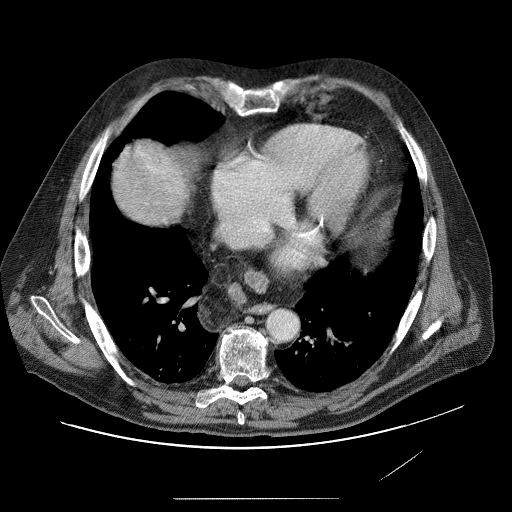
Contrast-enhanced abdominal CT (liver protocol), one axial slice; position 80 of 89 along the scan axis; soft-tissue window (W 400 / L 40 HU); 512 × 512 image matrix, field of view 420 × 420 mm. From the clinical record (not read from this slice): diagnosis: hepatocellular carcinoma (patient treated with transarterial chemoembolisation; whether this scan precedes or follows treatment is not stated here); TNM stage (as recorded): Stage-IVA.
Annotated regions visible in this slice (semi-automatically segmented with operator editing):
- liver parenchyma outside the tumour (the mass and vessels are separate outlines, so this box may not span the whole liver): bounding box <122,146,178,208> (left, top, right, bottom; pixels)
- mass: <147,161,174,189>